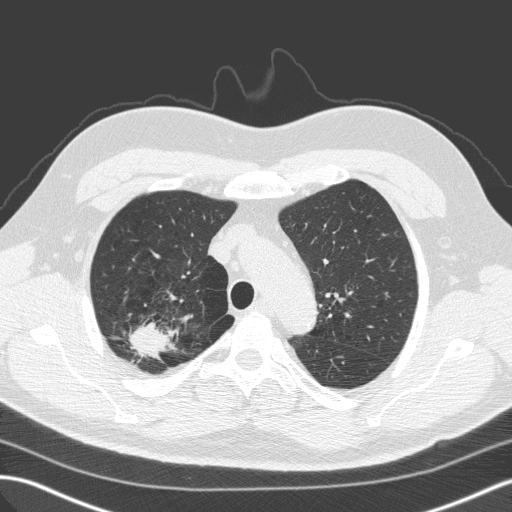
Low-dose screening chest CT, one axial slice. Slice 119 of 149 in the series (ordered by position). Lung window (W 1500 / L -600 HU). 2 mm slice thickness. 512 × 512 image matrix, field of view 357 × 357 mm.
Annotated regions visible in this slice (outlined manually by an expert reader):
- lesion 1 (tumor, upper lobe of right lung): box from (x=129, y=324) to (x=168, y=358) px